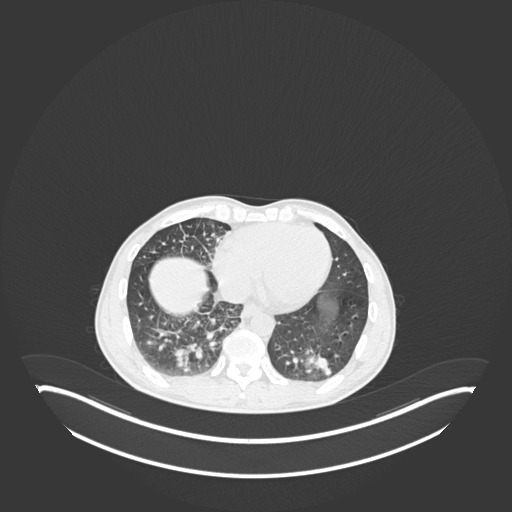
Chest CT, one axial slice. Position 66 of 237 along the scan axis. Reconstruction kernel B30f. Lung window (W 1500 / L -600 HU). 1 mm slice thickness. 512 × 512 image matrix, field of view 500 × 500 mm. Male patient, age 49 years. Case-level facts recorded for this patient, not image findings: clinical TNM (as recorded): T2b N1 M0.
Outlined on this slice (rectangle marked by the reading radiologist):
- lung tumour (recorded histology: adenocarcinoma): box from (x=291, y=346) to (x=335, y=382) px